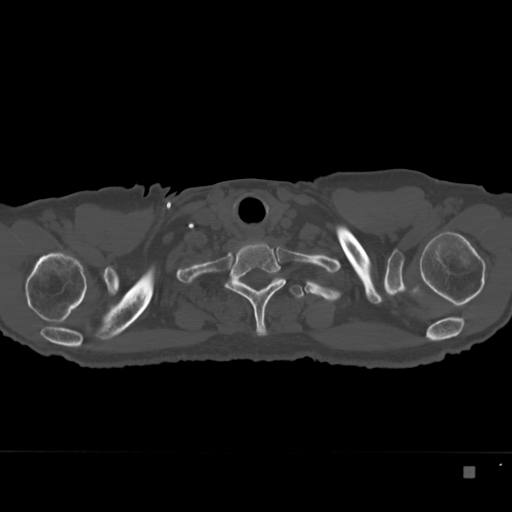
CT including the spine, one axial slice. Position 314 of 332 along the scan axis. Reconstruction kernel Br40s. Bone window (W 1800 / L 400 HU). 1.5 mm slice thickness. 512 × 512 image matrix, field of view 389 × 389 mm. Patient: male, 72 years. From the clinical record (not read from this slice): primary cancer: skeletal.
Structures marked on this image (semi-automatic segmentation, software-assisted and operator-edited):
- T1 vertebra: bounding box [x1, y1, x2, y2] px = [225, 241, 286, 336]
- T2 vertebra: [239, 277, 304, 299]